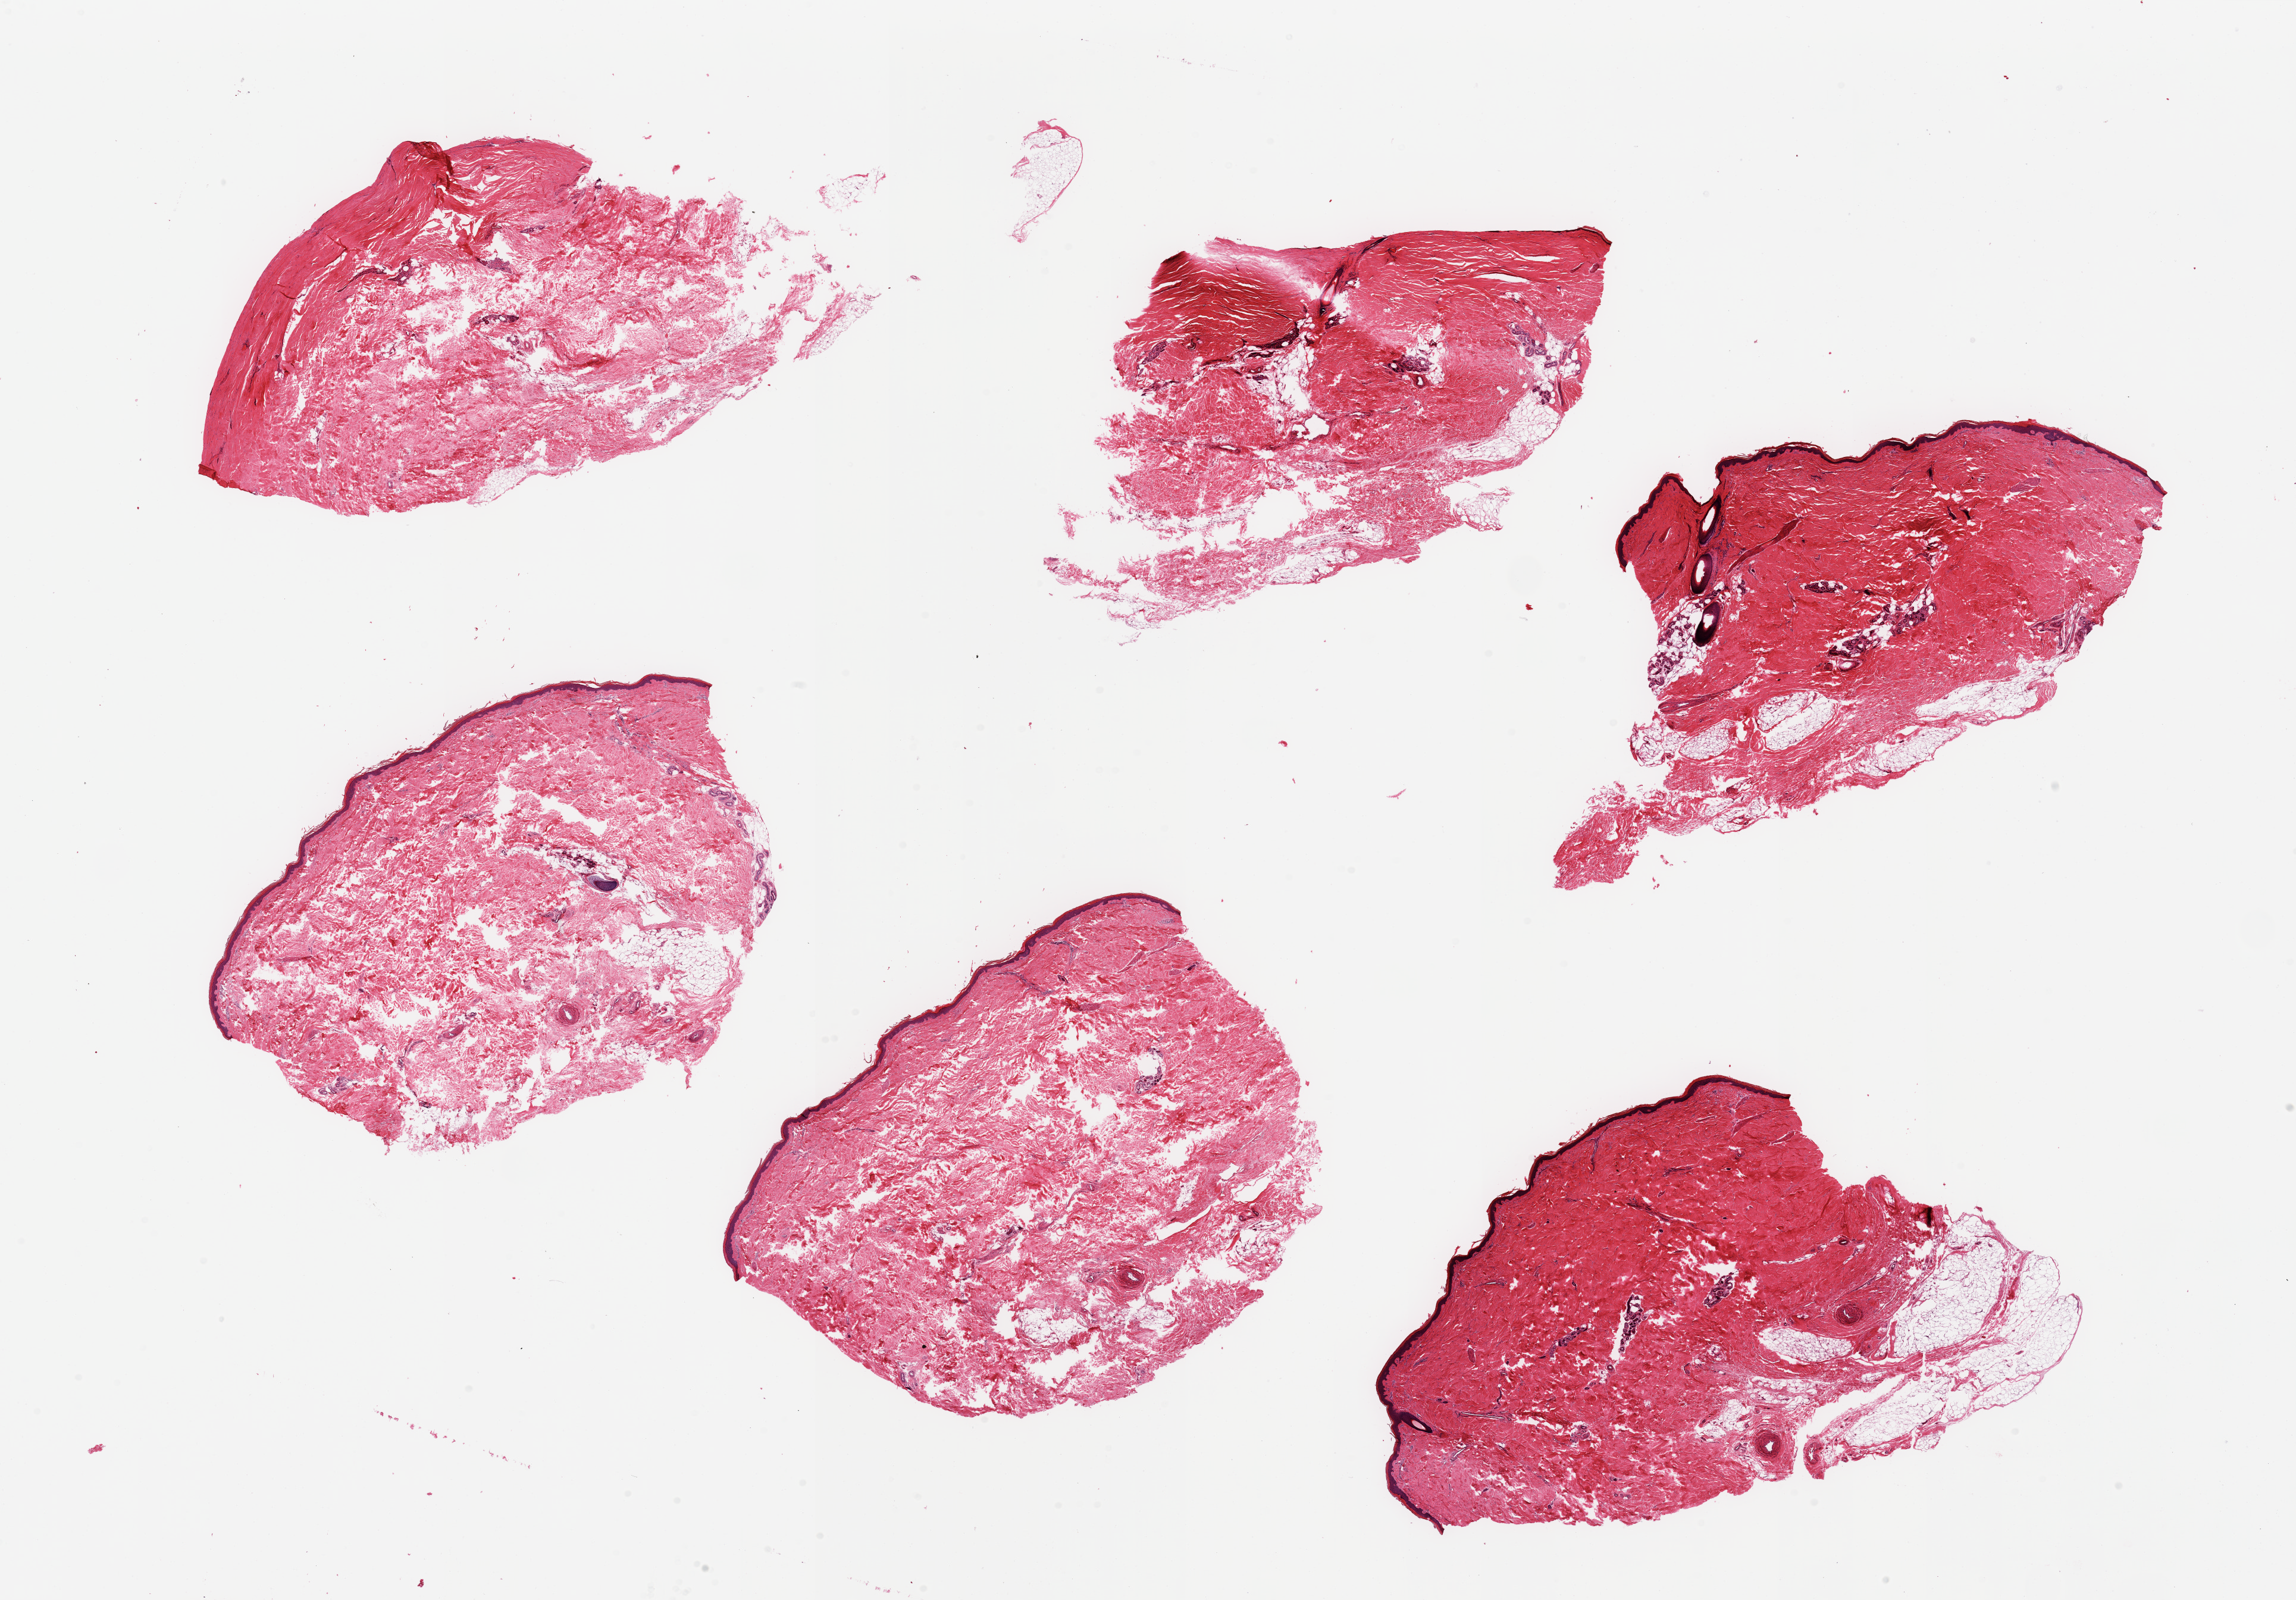
Hematoxylin and eosin (H&E) whole-slide image, brightfield — a low-resolution overview of the entire scanned area, about 30.5 x 21.3 mm, PAXgene-fixed, paraffin-embedded tissue, target tissue: skin of lower leg, donor tissue sample. Donor: male.
* reviewer comment on this tissue sample: 6 pieces; 2 pieces have sloughed epidermis; subcutaneous fat up to 2mm thick